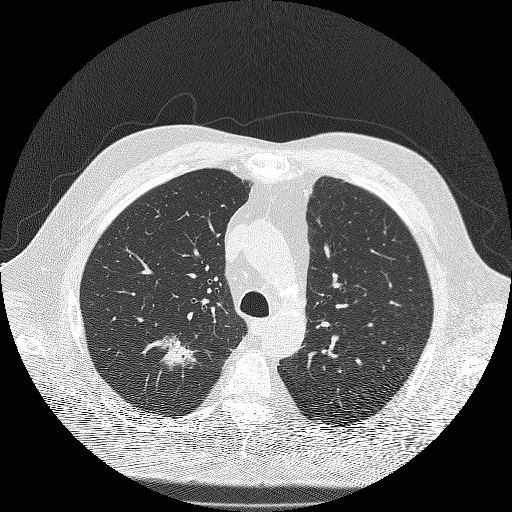
Low-dose screening chest CT, one axial slice. Position 142 of 180 along the scan axis. 120 kVp. Lung window (W 1500 / L -600 HU). 2 mm slice thickness. 512 × 512 image matrix, field of view 385 × 385 mm.
Annotated regions visible in this slice (expert manual segmentation):
- lesion 1 (tumor, upper lobe of right lung): bounding box <161,336,197,370> (left, top, right, bottom; pixels)